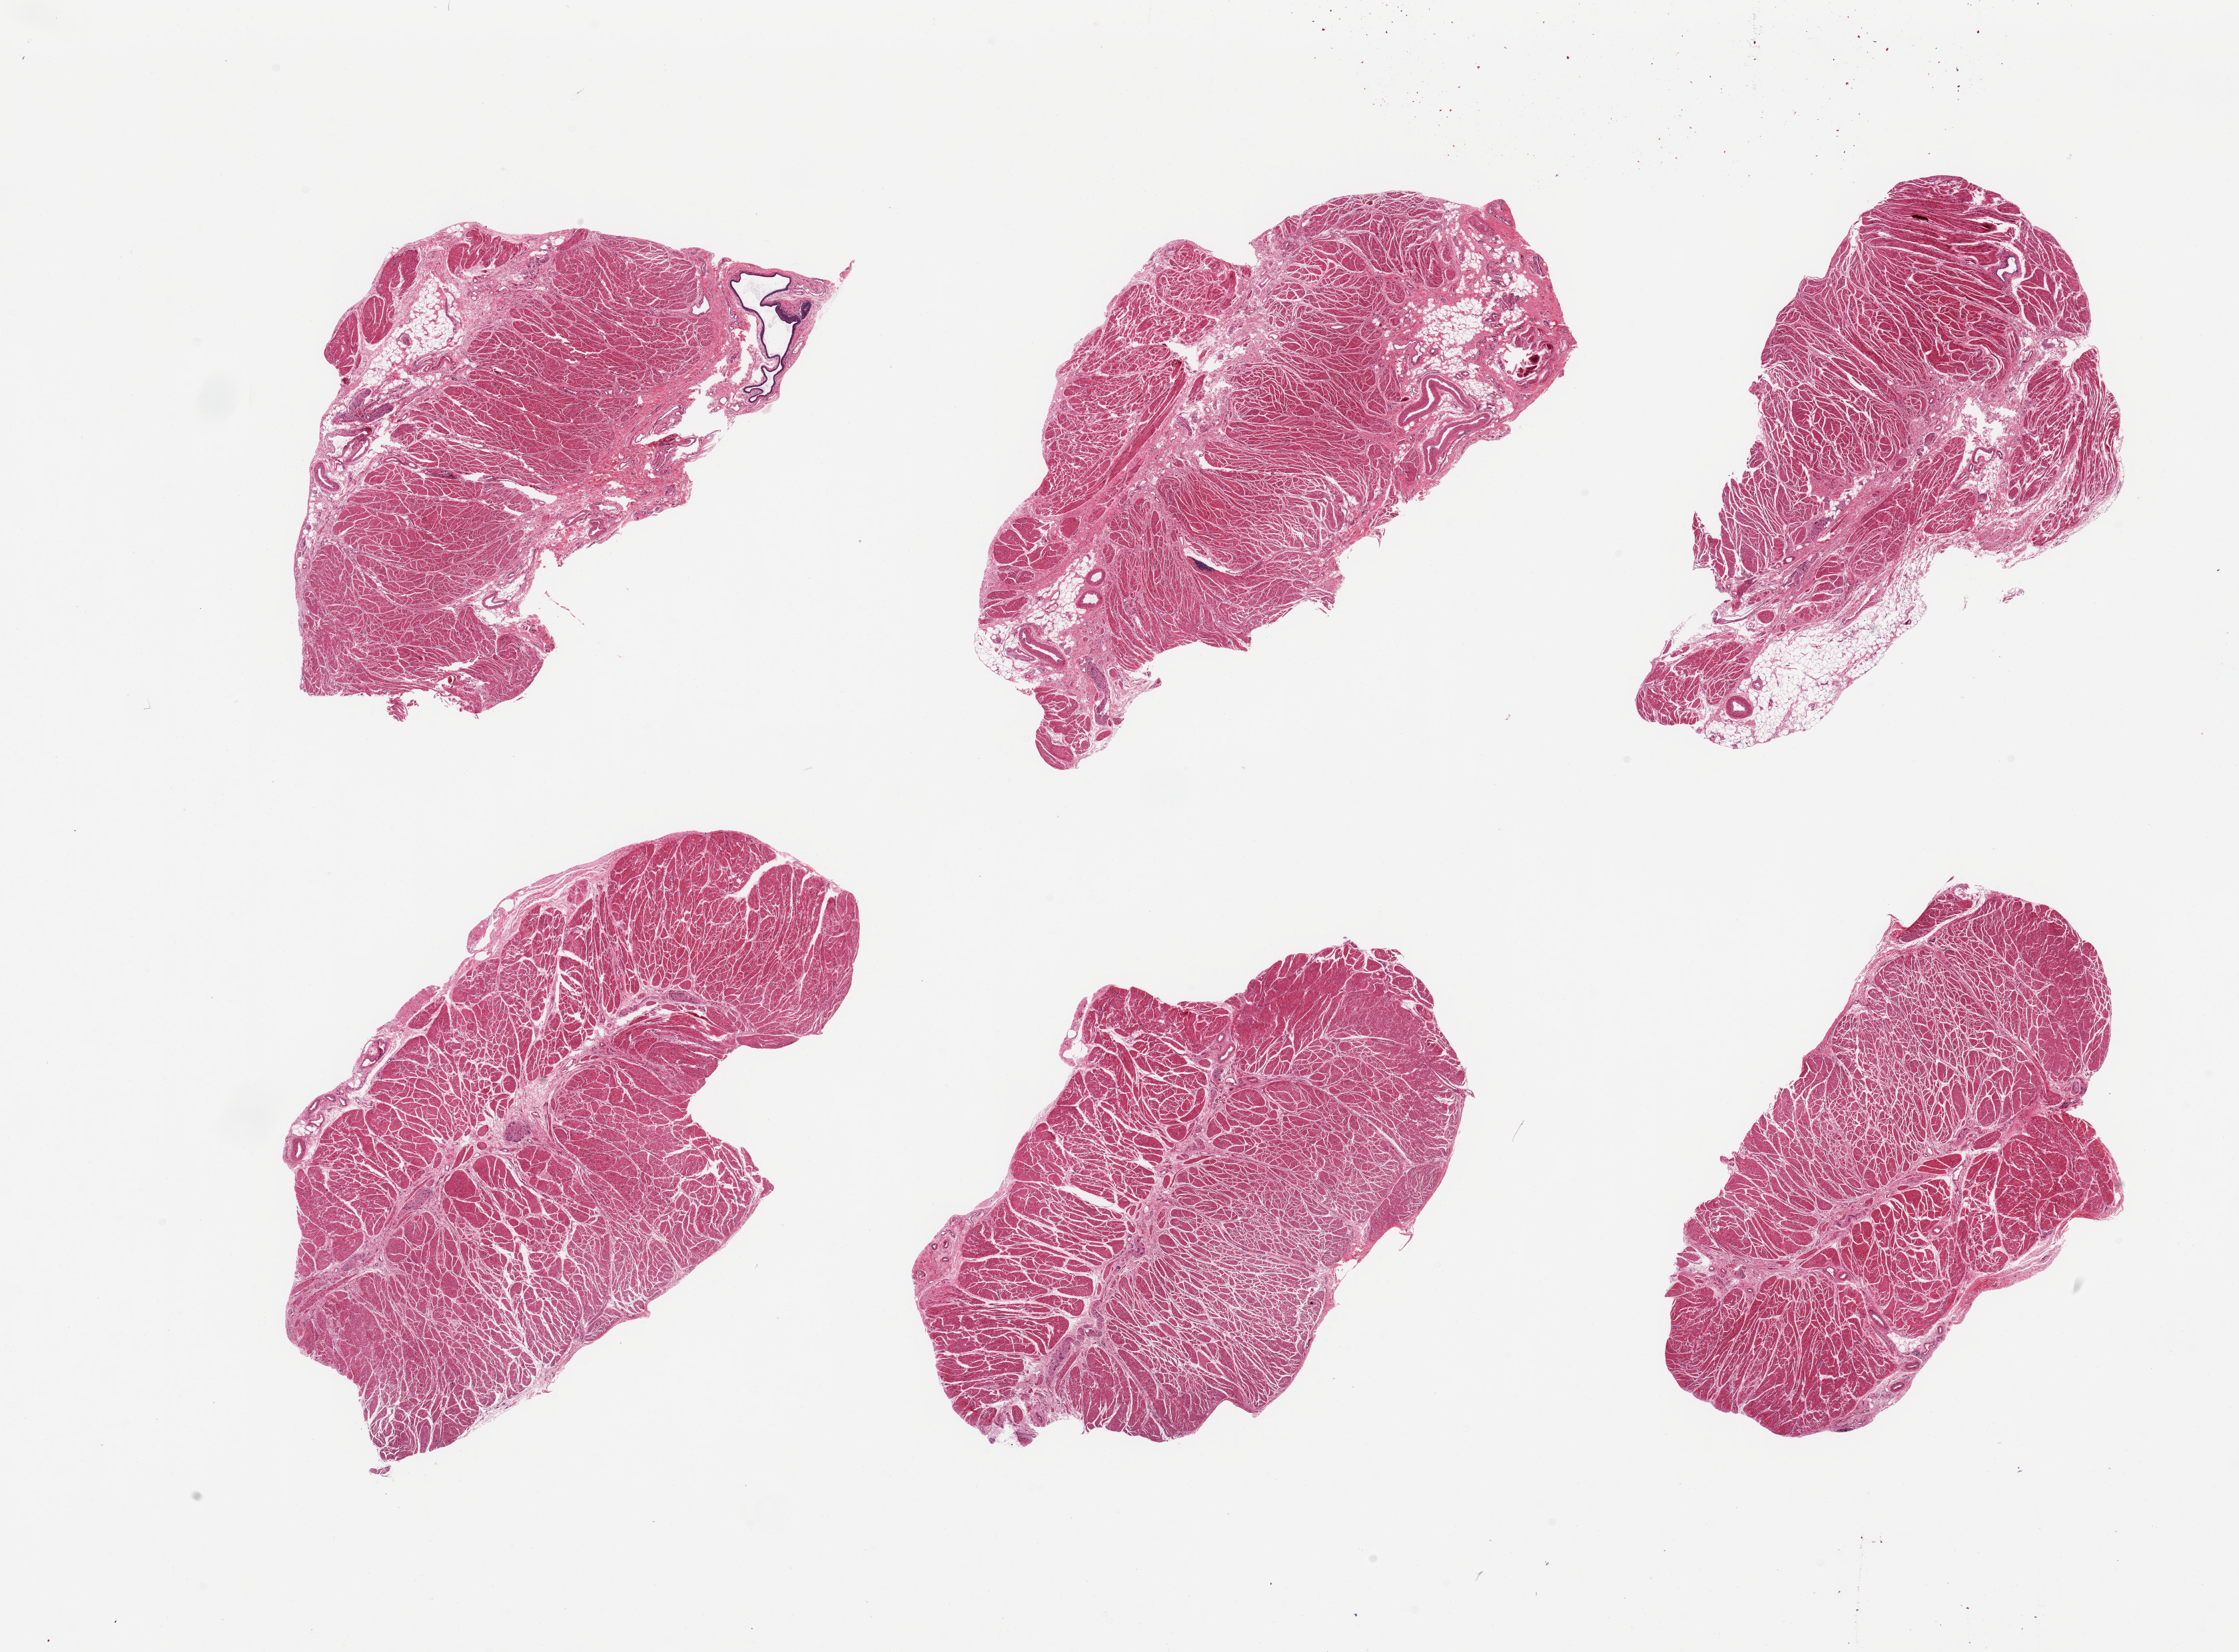
Hematoxylin and eosin (H&E) whole-slide image, shown as a low-resolution overview of the whole scanned area (about 26.6 x 19.6 mm), PAXgene-fixed paraffin-embedded (PFPE) section, section of gastroesophageal junction (target tissue), tissue donor sample. Male donor.
- pathologist's review note for this sample: 6 pieces, confirmed target muscularis